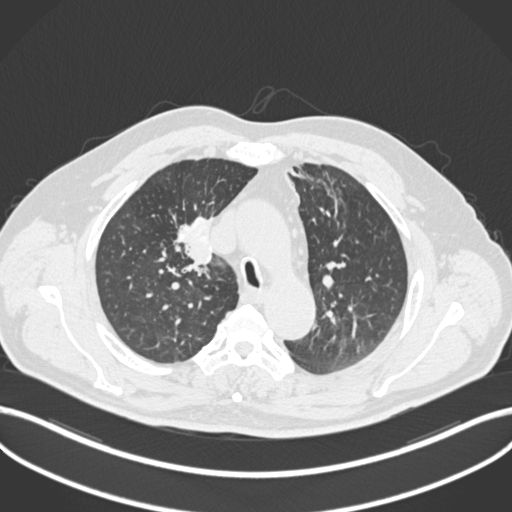
Chest CT, one axial slice. Slice 142 of 255 in the series (ordered by position). Reconstruction kernel B30f. 120 kVp. Lung window (W 1500 / L -600 HU). 1 mm slice thickness. 512 × 512 image matrix, field of view 400 × 400 mm. Male patient, age 60 years. Case-level facts recorded for this patient, not image findings: clinical TNM (as recorded): T1b N1 M0.
Outlined on this slice (bounding box drawn by a radiologist):
- lung tumour (recorded histology: squamous cell carcinoma): bounding box <171,213,226,274> (left, top, right, bottom; pixels)